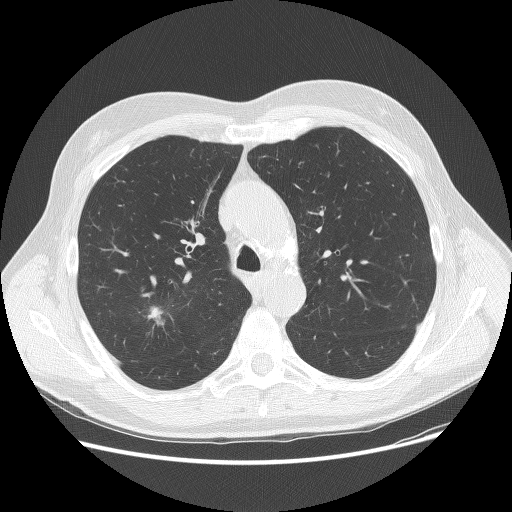
Low-dose screening chest CT, axial slice. Baseline screening round. Lung window (W 1500 / L -600 HU). 2.5 mm slice thickness. 120 kVp. 512 × 512 image matrix, field of view 380 × 380 mm. Male, age 70 years at enrolment. Current smoker at enrolment.
Expert-annotated lung lesion, bounding box [x1, y1, x2, y2] px = [129, 284, 192, 340]. The screening reader recorded 2 non-calcified nodules or masses ≥4 mm on this exam (right upper lobe, left lower lobe); which of them this box marks is not recorded. Official screen result: positive, change unspecified: nodule(s) >= 4 mm or enlarging nodule(s), mass(es), or other non-specific abnormalities suspicious for lung cancer. Later outcome: lung cancer diagnosed 15 days after this screen — adenocarcinoma, NOS, right upper lobe, poorly differentiated (G3), stage IIA (AJCC 6th edition), 23 mm at pathology.